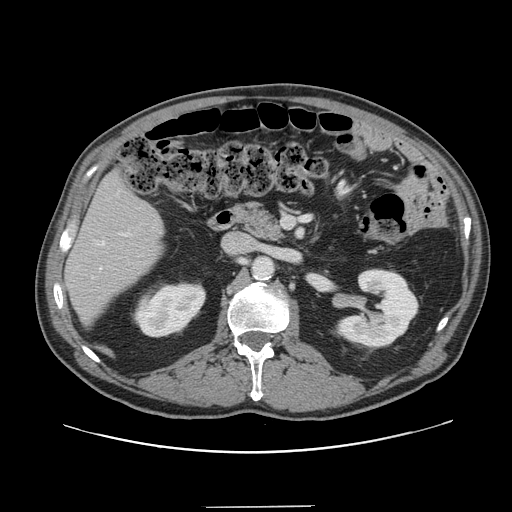
Contrast-enhanced abdominal CT, one axial slice; position 67 of 139 along the scan axis; soft-tissue window (W 400 / L 40 HU); 2.5 mm slice thickness; 512 × 512 image matrix, field of view 397 × 397 mm. Male patient, age 64 years. From the clinical record (not read from this slice): diagnosis: colorectal cancer liver metastases, imaged before liver resection.
Outlined on this slice (outlined manually by an expert reader):
- hepatic veins: box from (x=100, y=242) to (x=105, y=270) px
- liver: (x=66, y=175)–(x=162, y=322)
- planned liver remnant (the part of the liver to remain after resection): (x=67, y=176)–(x=162, y=322)
- portal vein (with intrahepatic branches): (x=123, y=233)–(x=129, y=236)